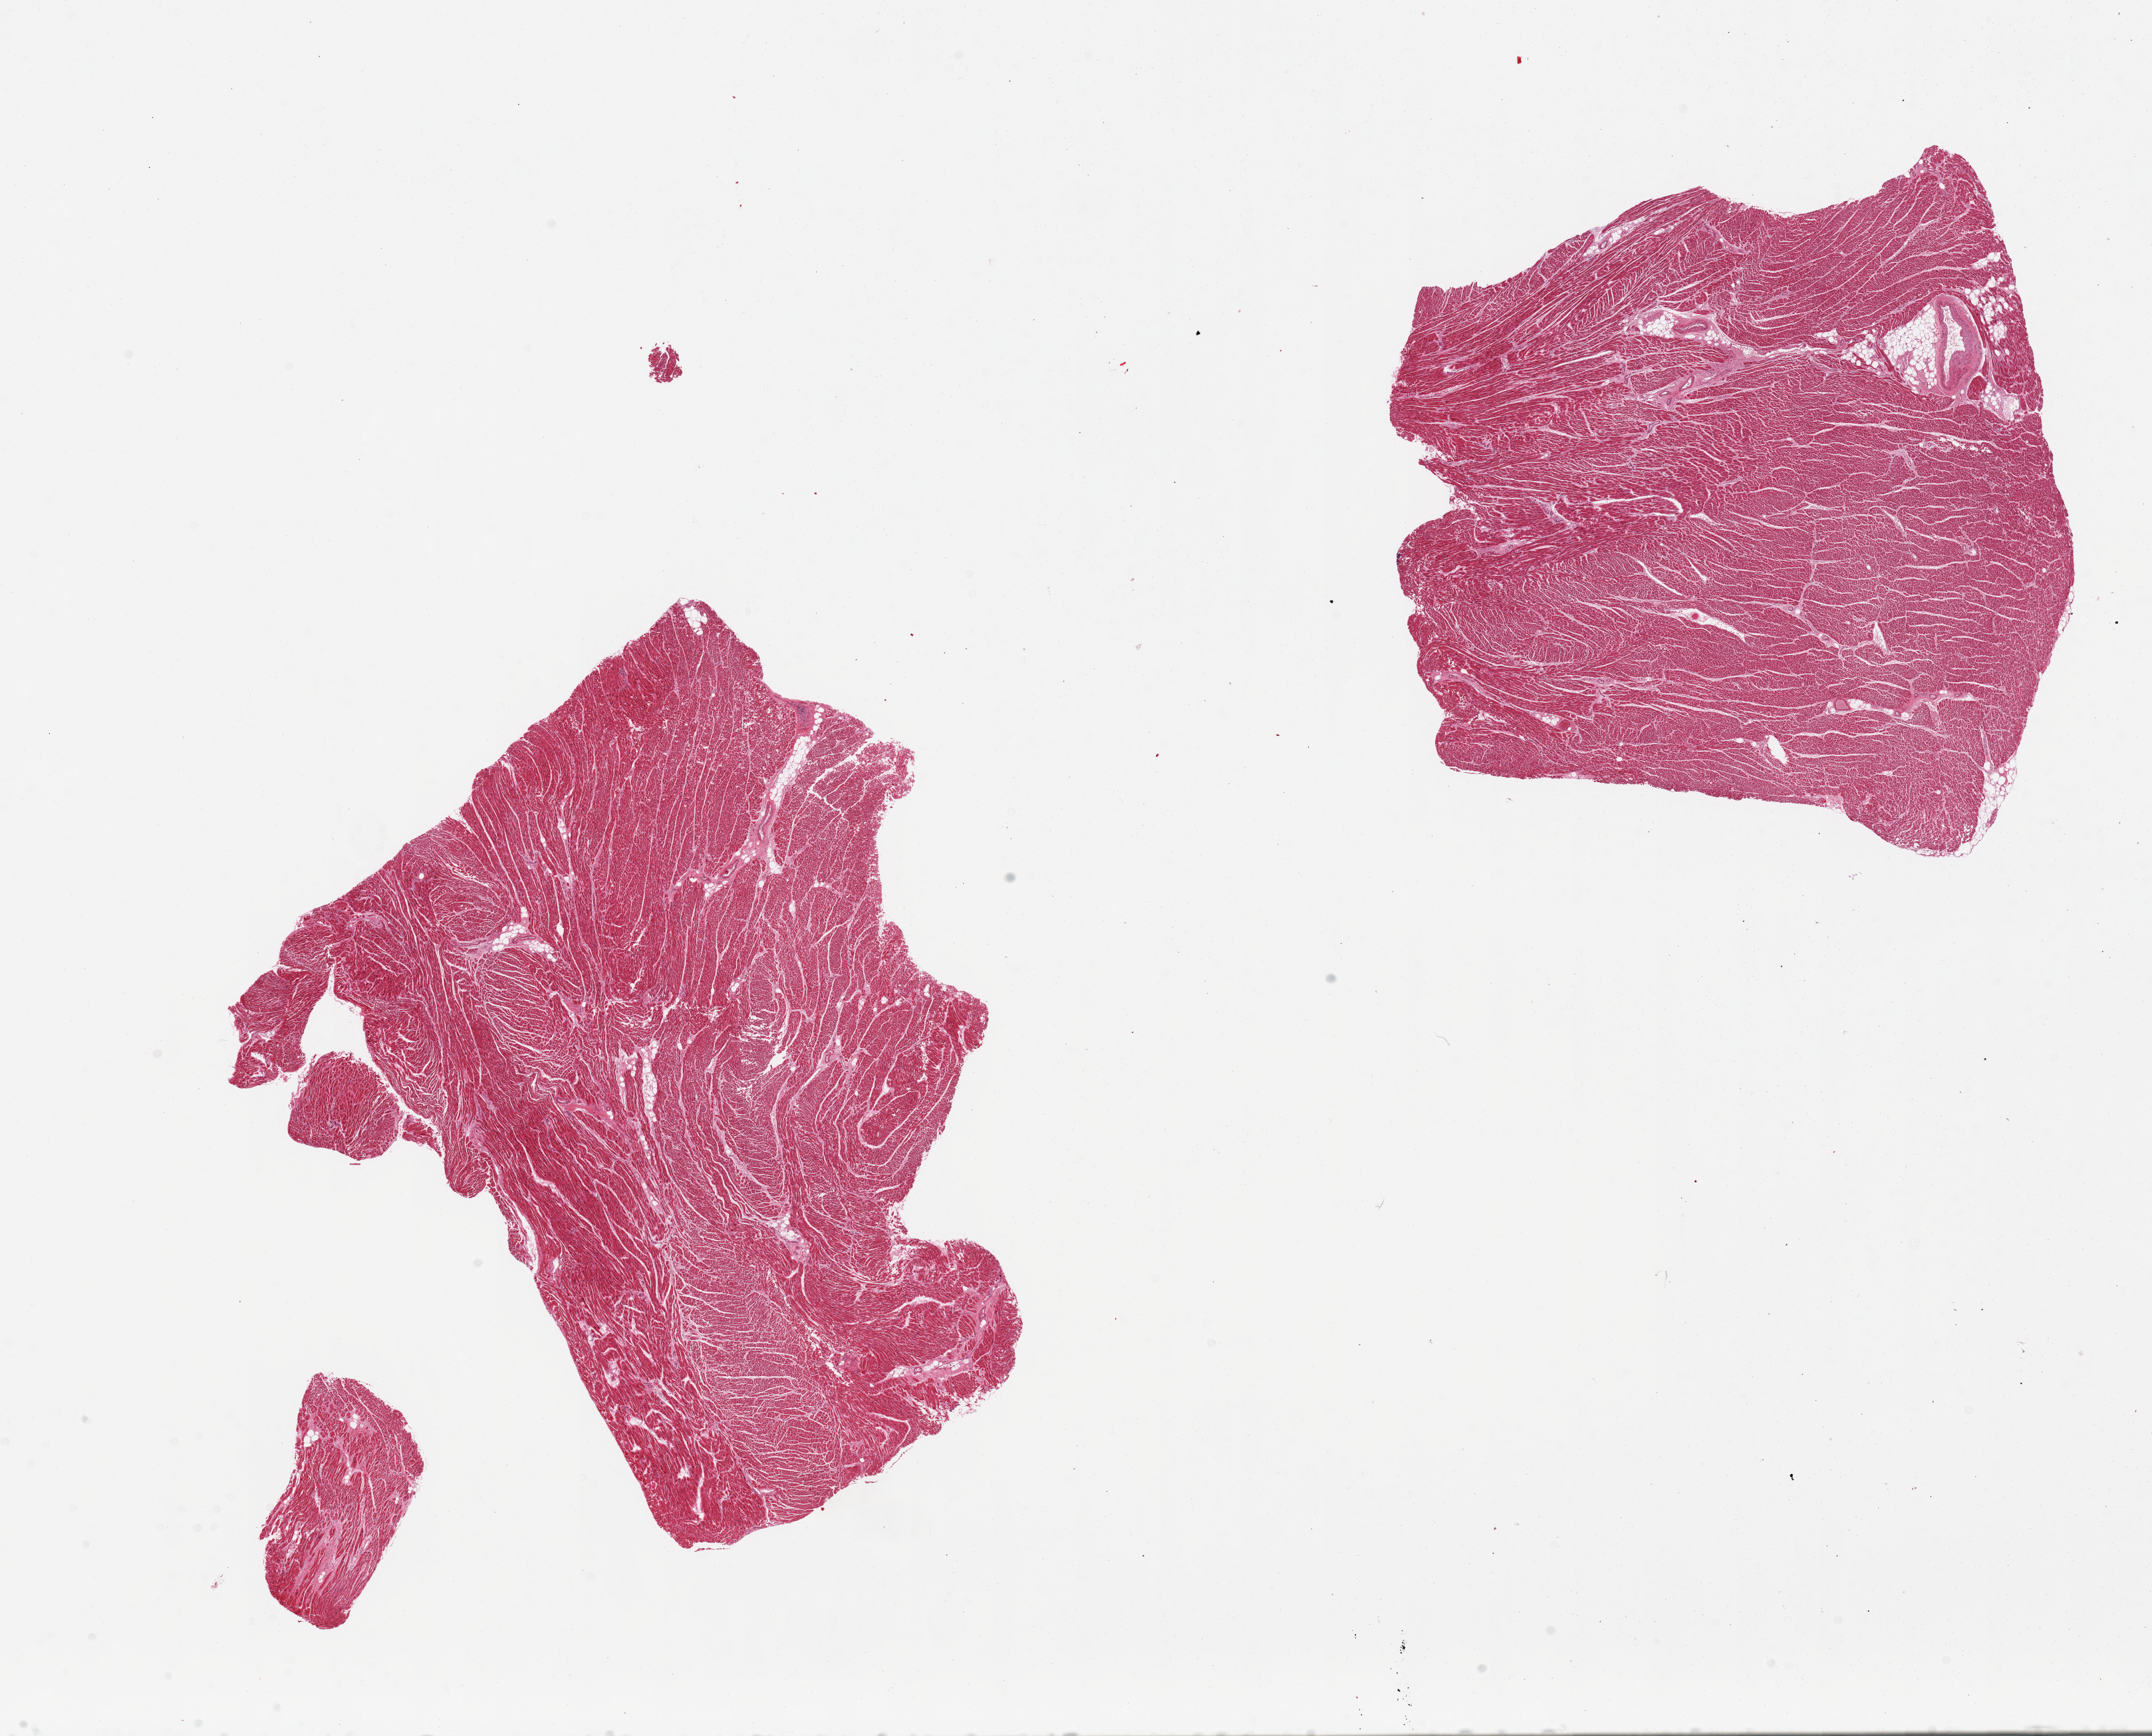
Whole-slide image, haematoxylin and eosin stain, brightfield, whole scanned area (about 25.6 x 20.6 mm) shown as a low-resolution overview, PAXgene-fixed, paraffin-embedded tissue, section of heart (target tissue), donor tissue sample.
Review note (as recorded): 2 pieces, no significant fibrosis, intracardiac coronary artery (~1mm d.).